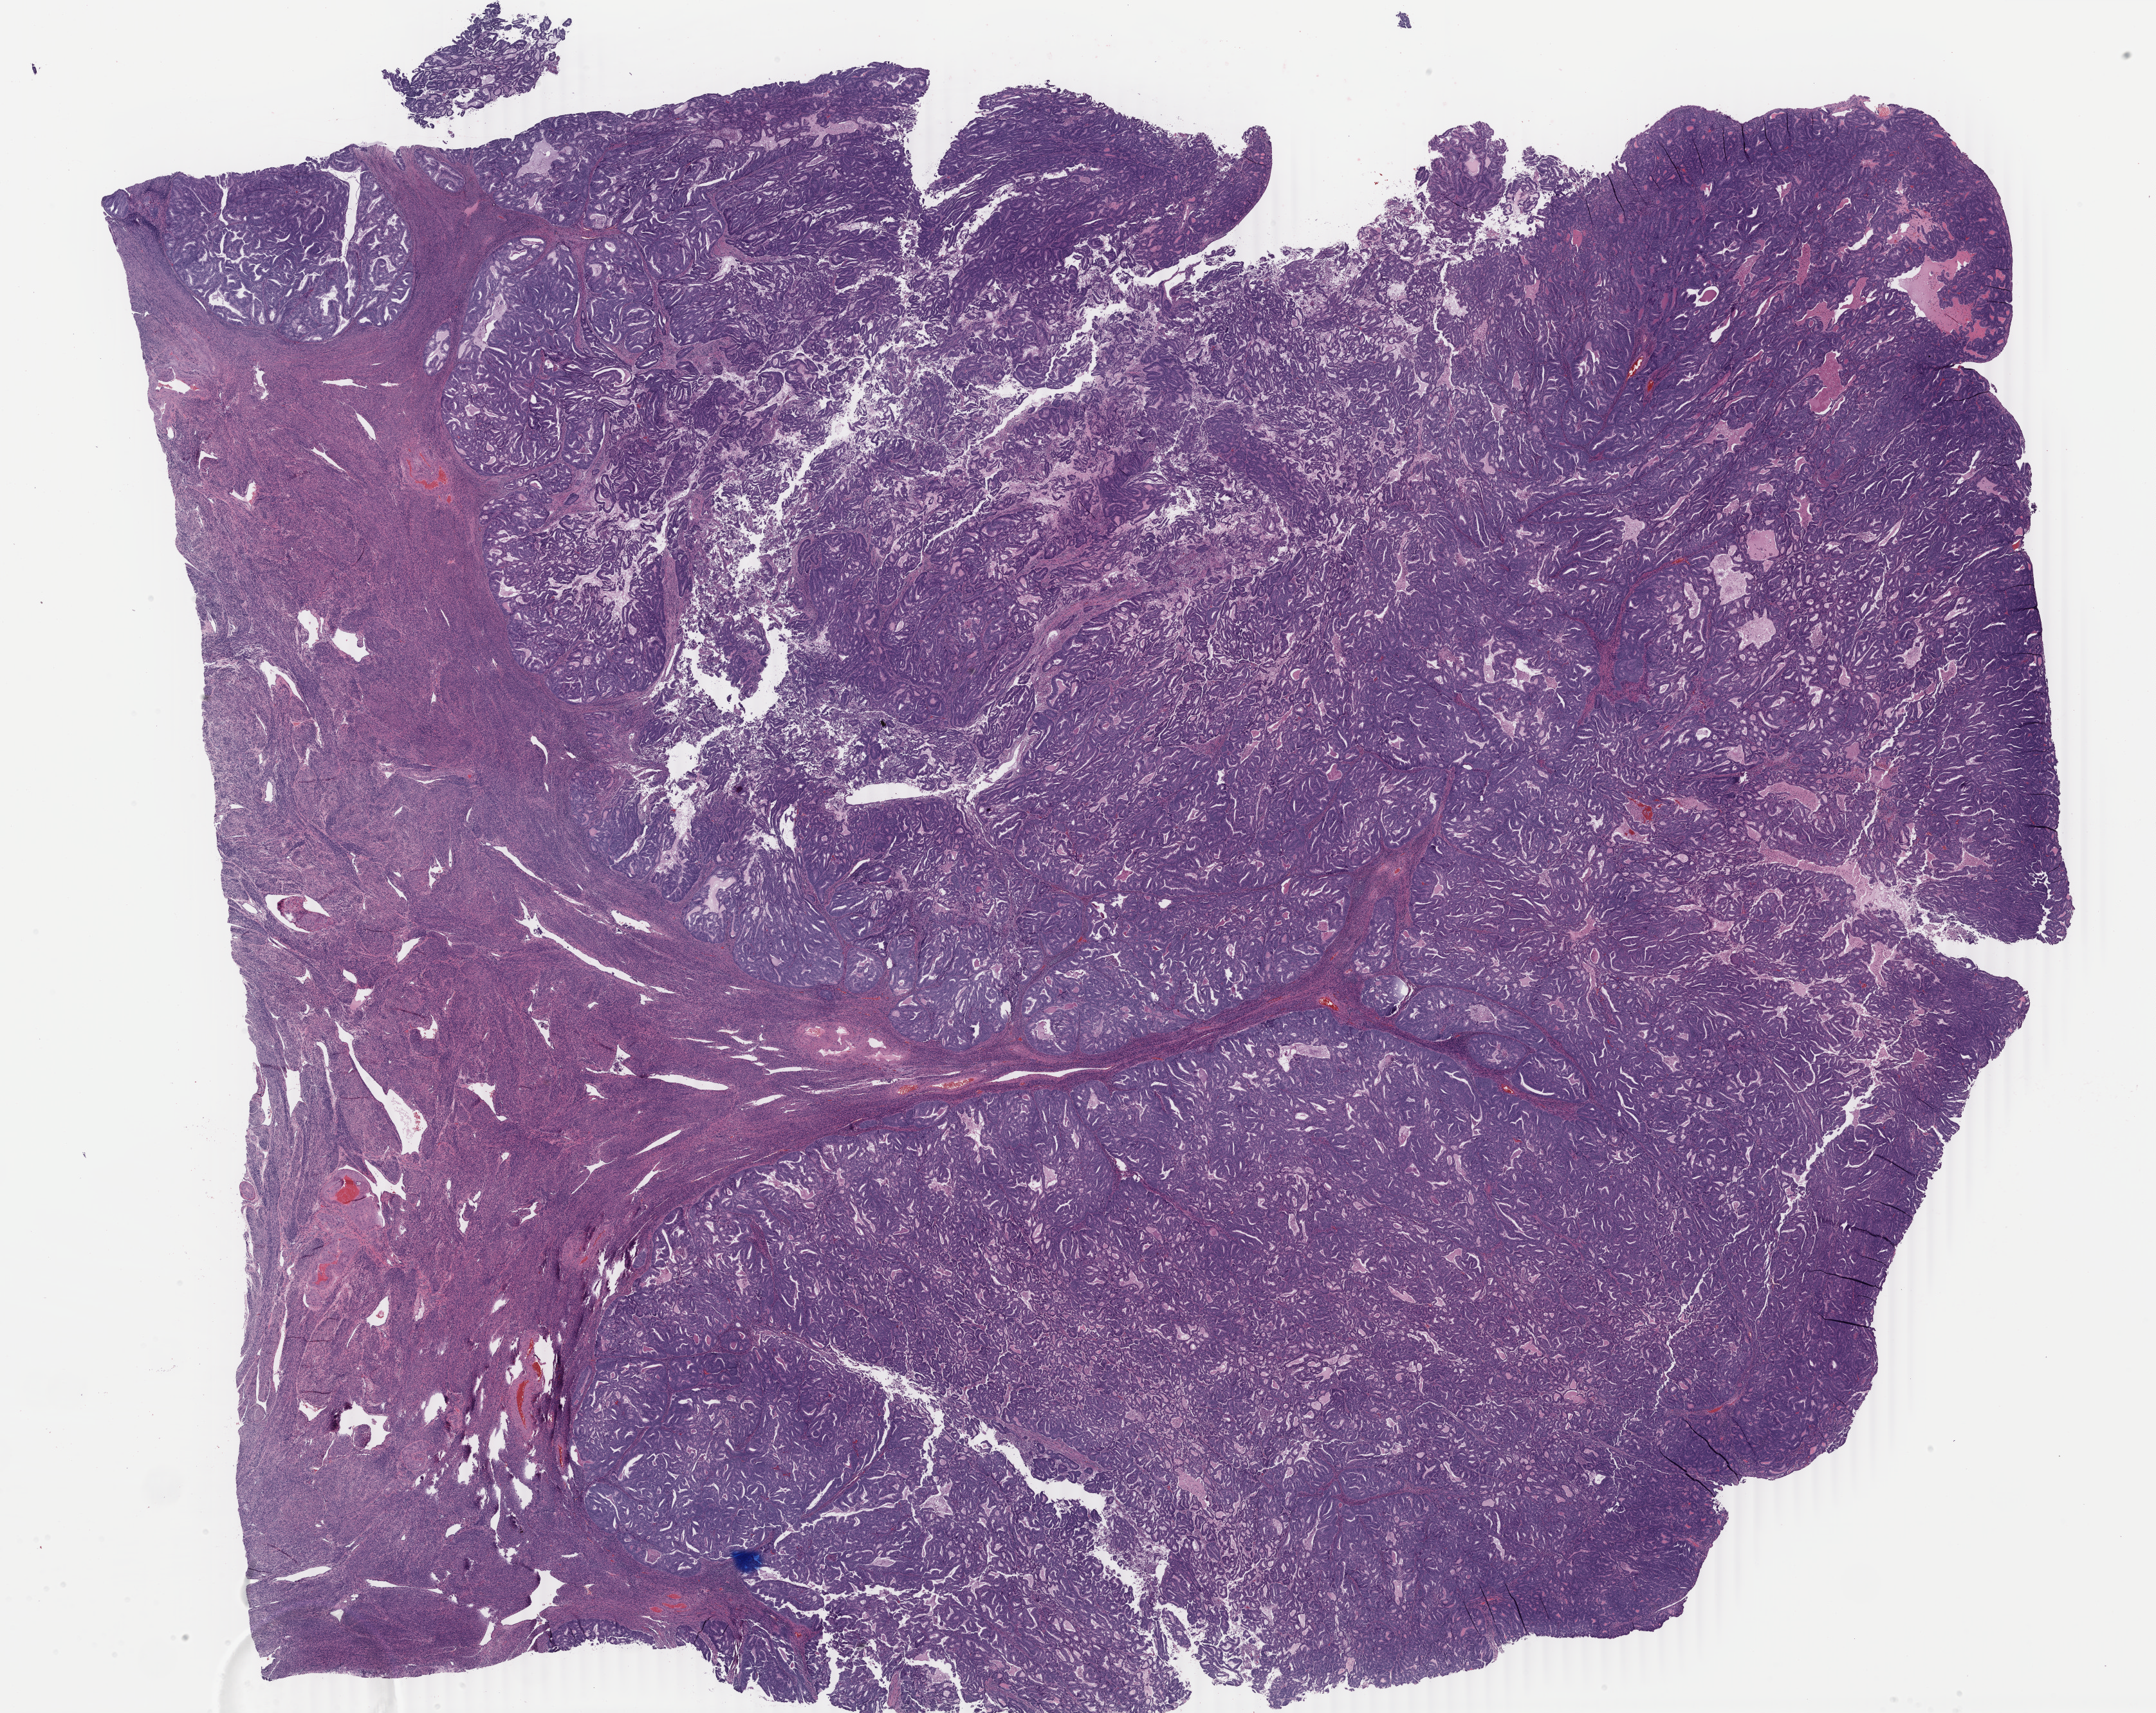
H&E whole-slide image — whole scanned area (about 26.7 x 21.2 mm) shown as a low-resolution overview. Formalin-fixed paraffin-embedded (FFPE) diagnostic section. Sample: primary tumour, uterus. Female, age 61 years at initial diagnosis. Histologic grade: G2 (moderately differentiated).
Pathologic diagnosis: Endometrioid adenocarcinoma, NOS (endometrium). FIGO stage: IIIA.